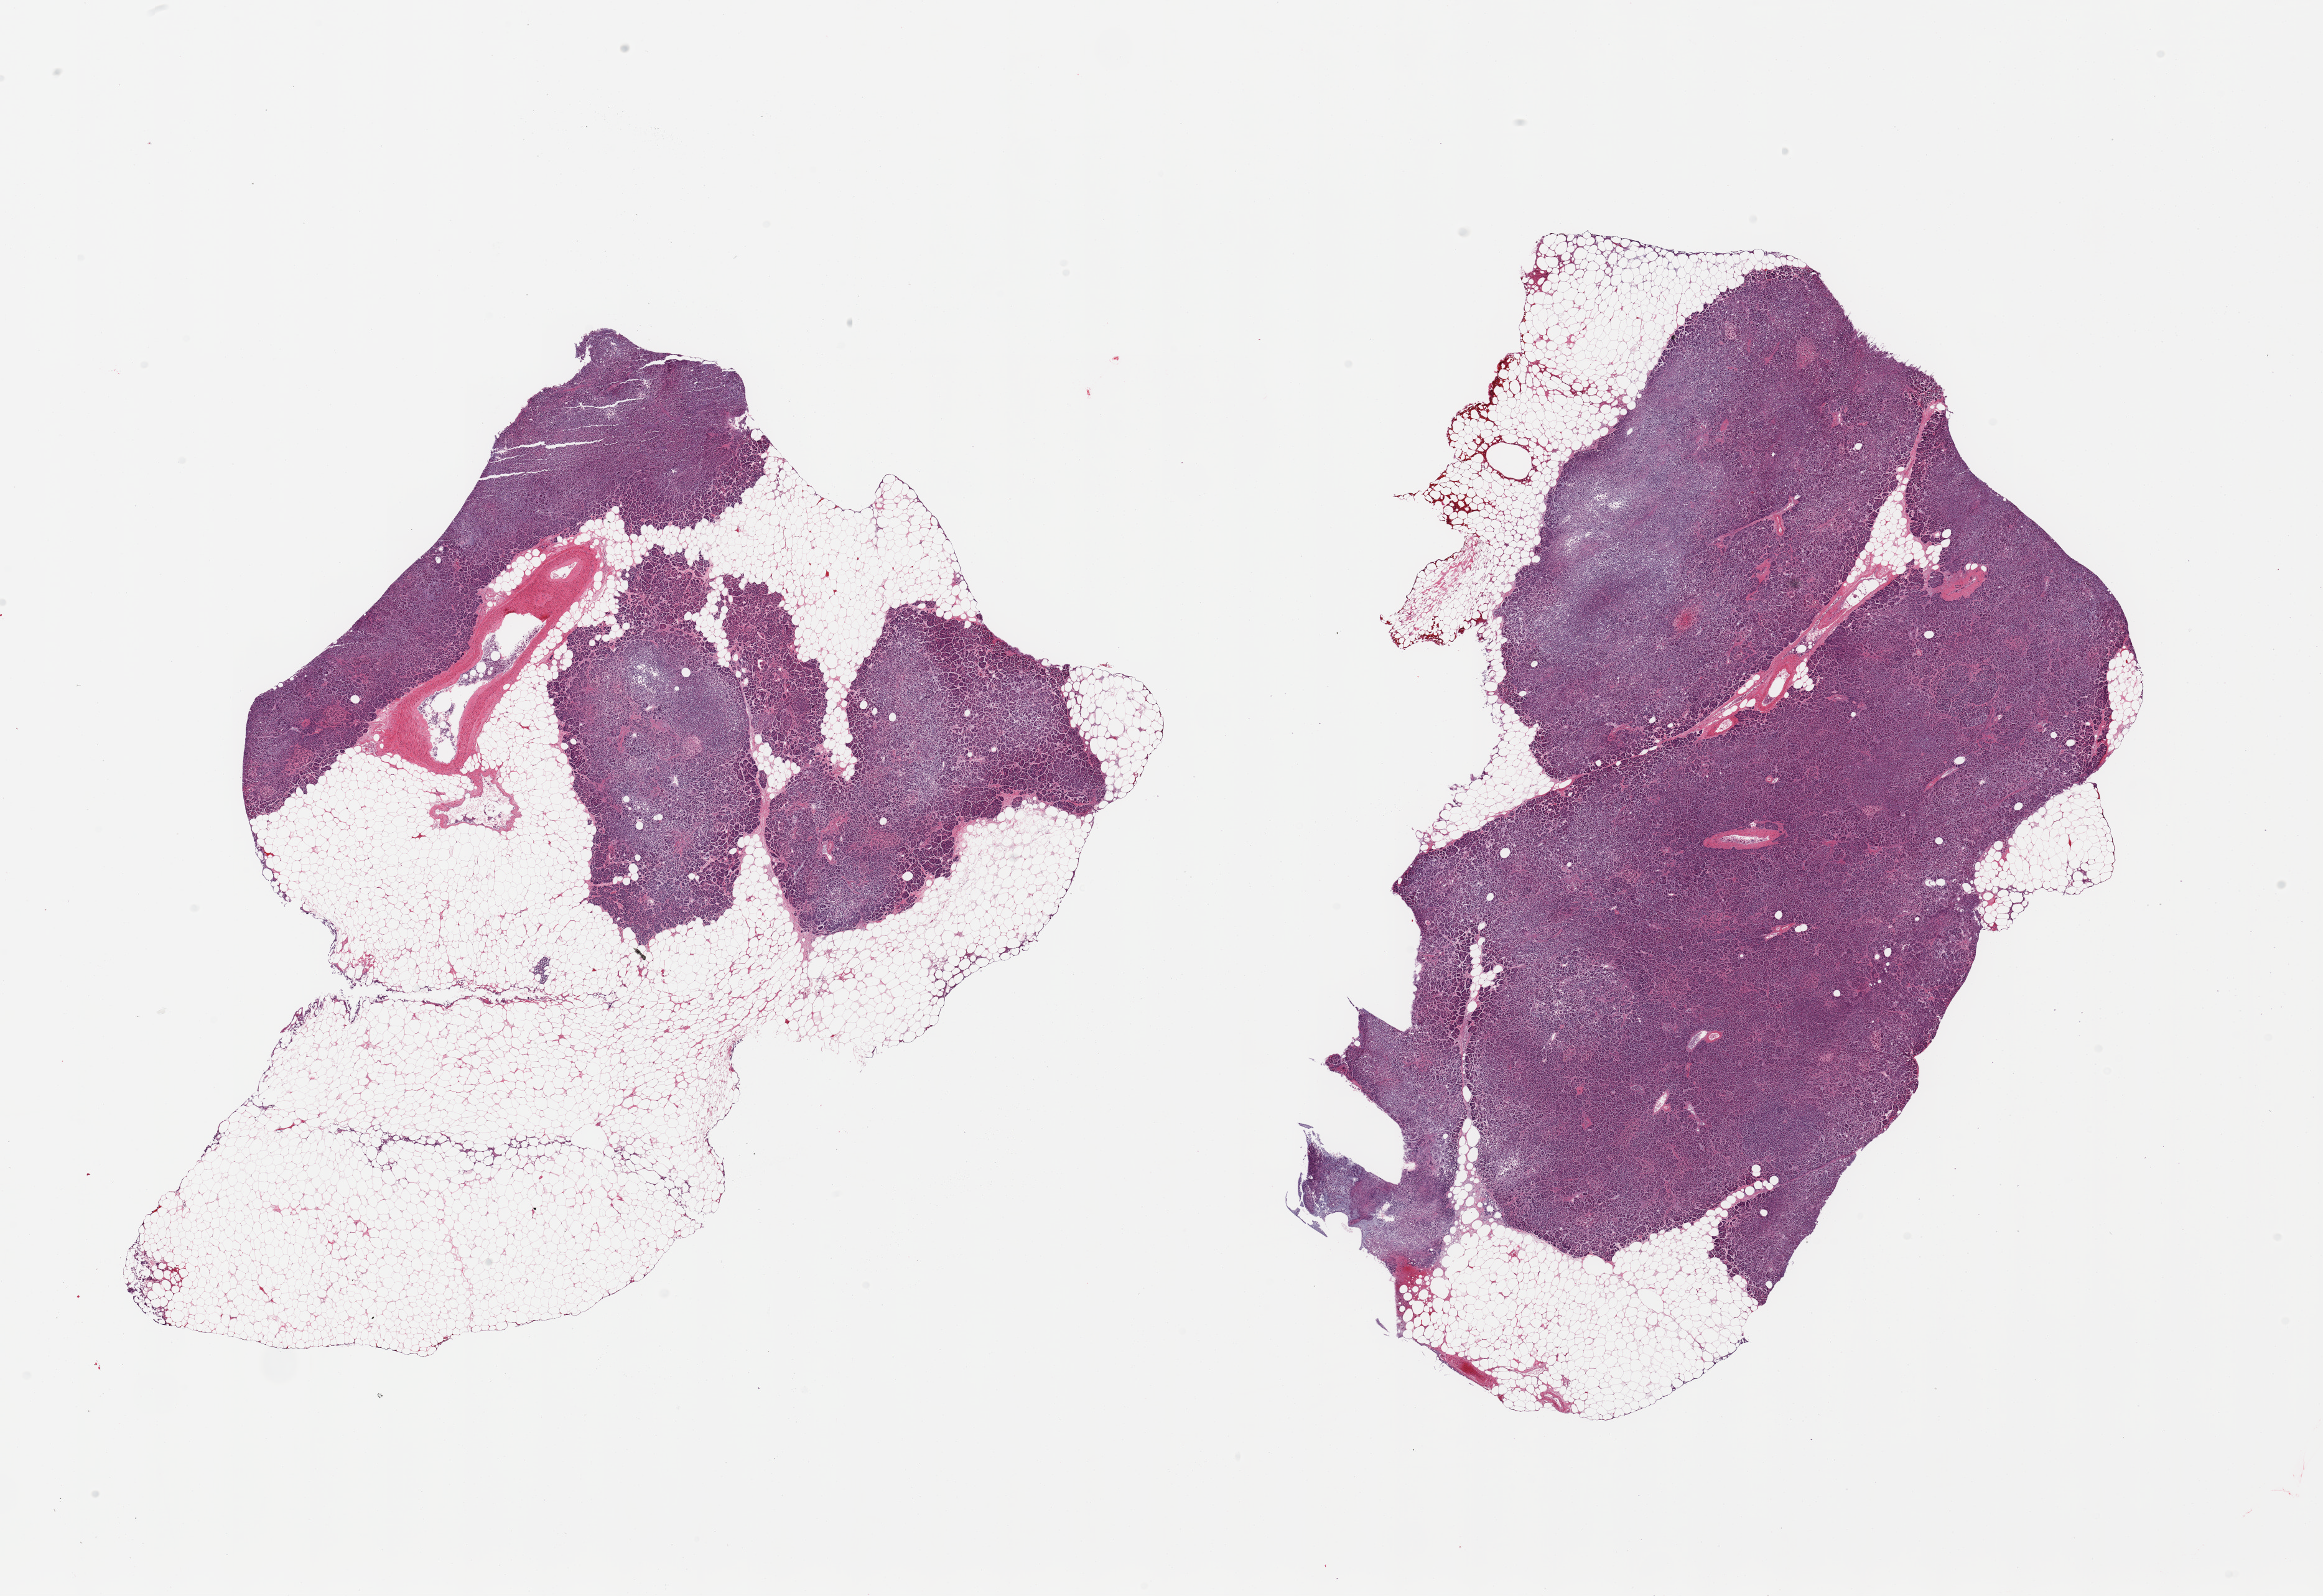
Hematoxylin and eosin (H&E) whole-slide image — shown as a low-resolution overview of the whole scanned area (about 29.5 x 20.3 mm, slide scanned at 20x), PAXgene-fixed paraffin-embedded (PFPE) section, target tissue: pancreas, donor tissue sample.
• reviewer comment on this tissue sample: 2 pieces, moderately advanced saponification; islets badly degraded; ~40% interstitial fat